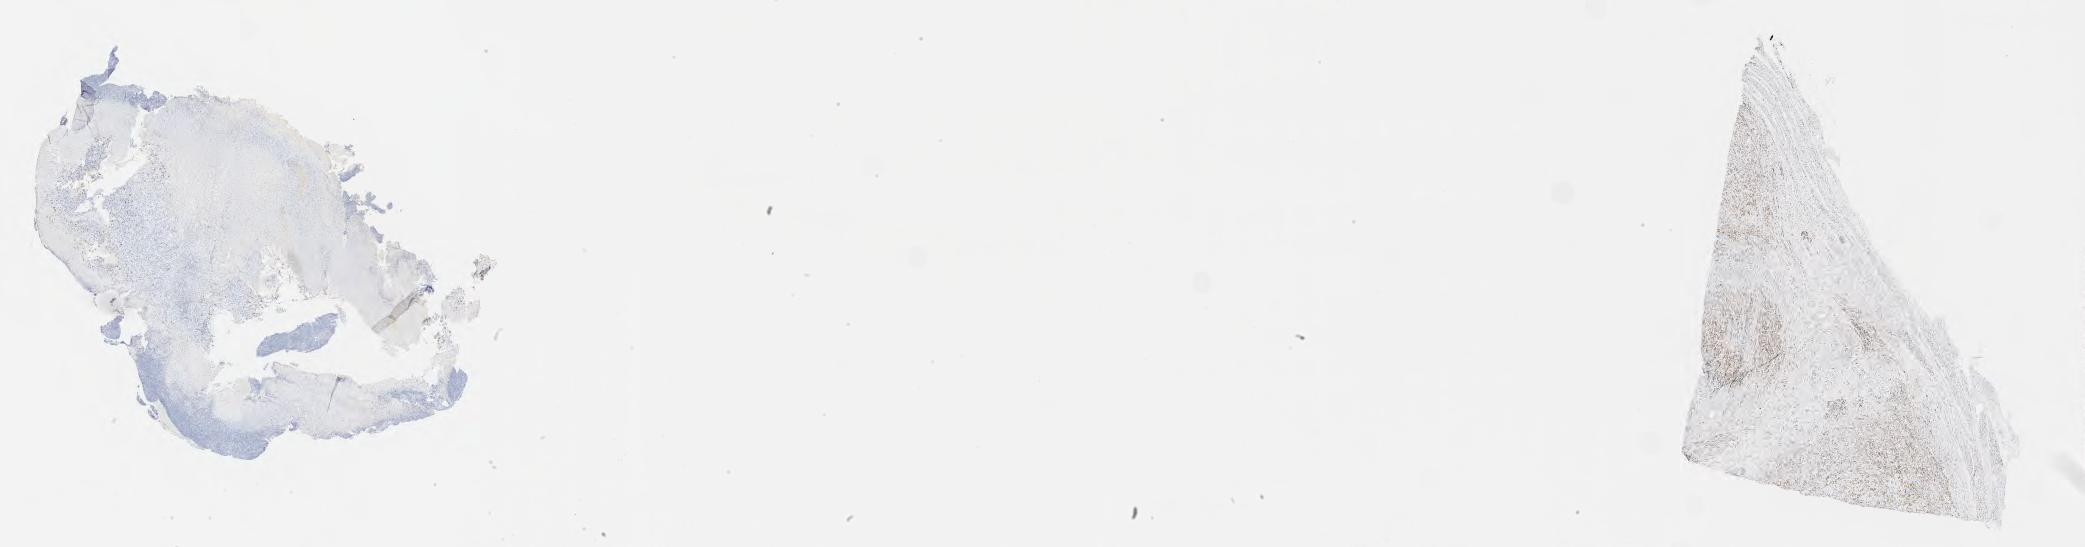
IHC for progesterone receptor (PR), whole-slide image — whole scanned area (about 33.7 x 8.8 mm) shown as a low-resolution overview. Tumor tissue. Site: cervix. Patient: female, 62 years old.
Histologic diagnosis: Squamous cell carcinoma, large cell, nonkeratinizing, NOS.